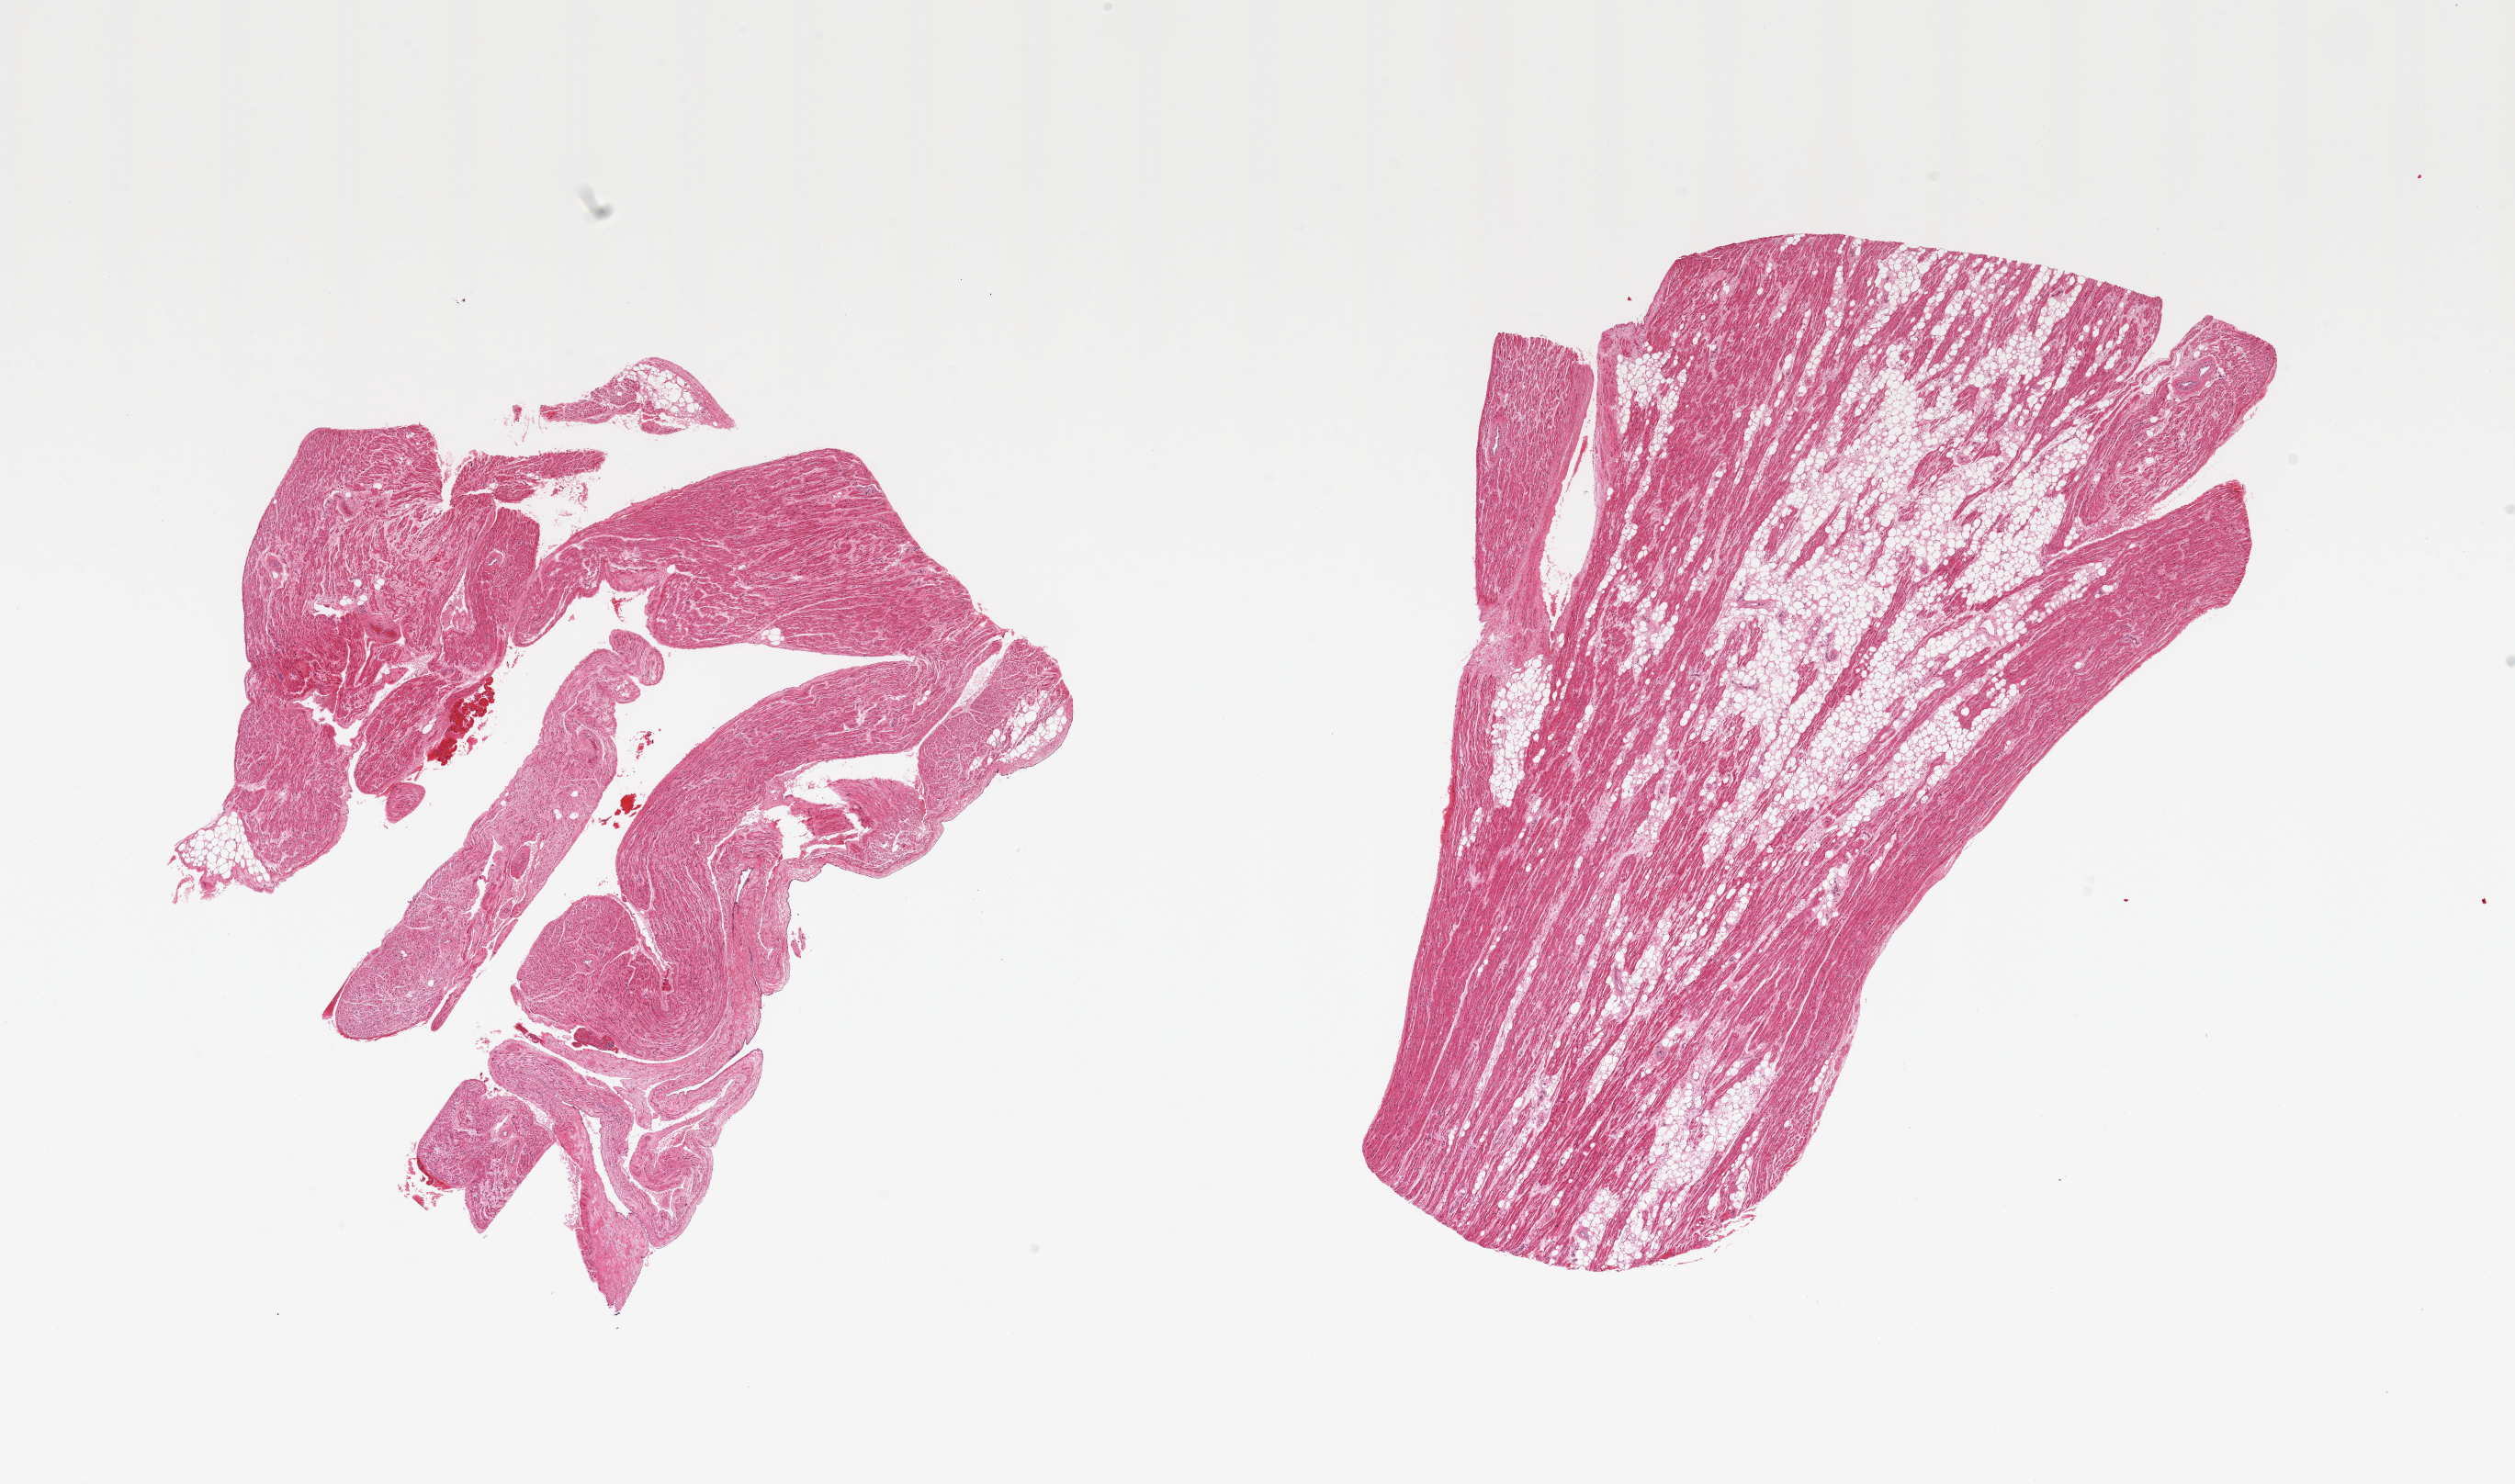
Digitized H&E-stained section, low-resolution overview of the scanned area, about 21.7 x 12.8 mm. PAXgene-fixed paraffin-embedded (PFPE) section. Sampled site (target tissue): auricular appendage. Donor tissue sample. Male donor.
* pathologist's review note for this sample: 2 pieces, no abnormalites